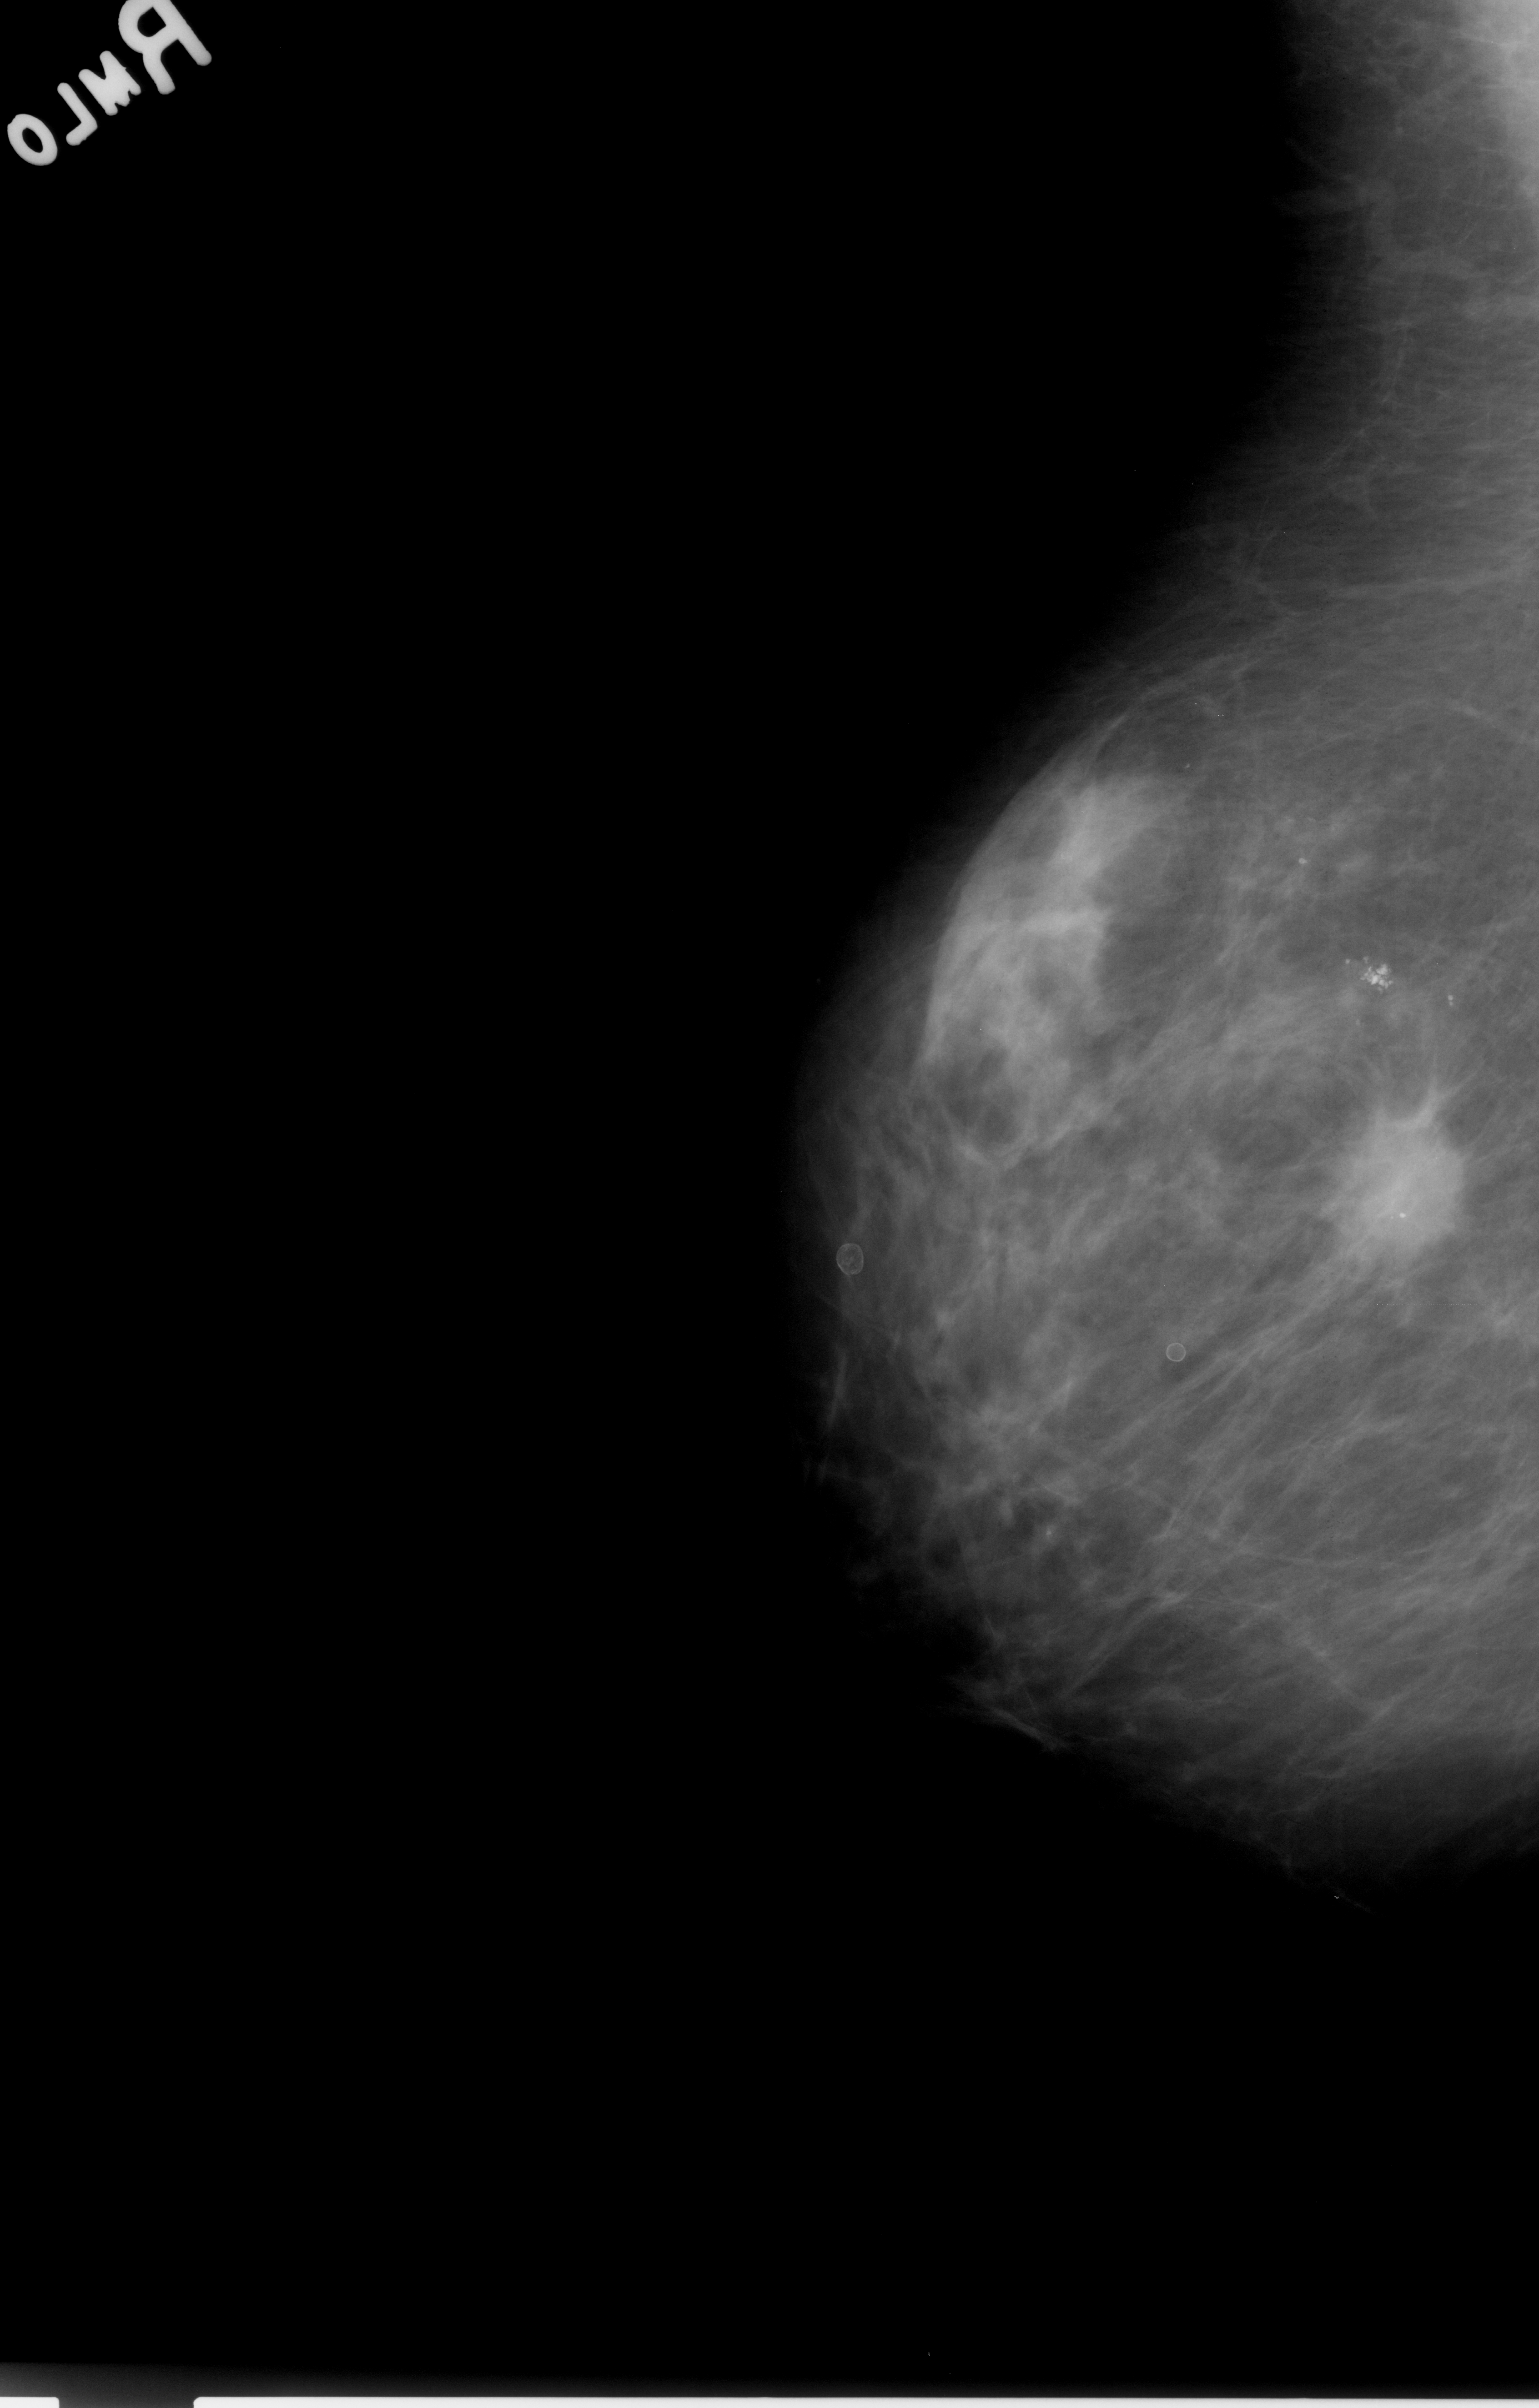
Scanned film-screen mammogram, right breast, MLO view, BI-RADS breast density category 2 (scale 1–4).
Radiologist-marked abnormalities on this image: mass, shape irregular / architectural distortion, margins spiculated; BI-RADS assessment category 4; subtlety rating 5 on a 1 (subtle) to 5 (obvious) scale; pathology (as recorded): malignant.